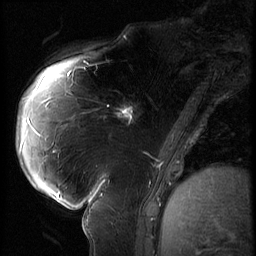
Breast MRI (dynamic contrast-enhanced), one sagittal slice; slice 22 of 62 in the series (ordered by position); 3 images stored at this slice position (order not interpretable as contrast timing); 1.5 T; TE 4.2 ms, TR 9 ms; 256 × 256 image matrix. Patient: female, 57 years. Case-level facts recorded for this patient, not image findings: setting: breast cancer imaged before/during neoadjuvant chemotherapy; receptor status: triple-negative.
Structures marked on this image (semi-automatically segmented with operator editing):
- analysis volume of interest (the breast-tissue region the enhancement analysis was run in; not a lesion): box from (x=105, y=84) to (x=158, y=135) px
- tumour enhancement mask (voxels above the 140 % enhancement threshold inside the analysis volume of interest): (x=108, y=106)–(x=134, y=123)